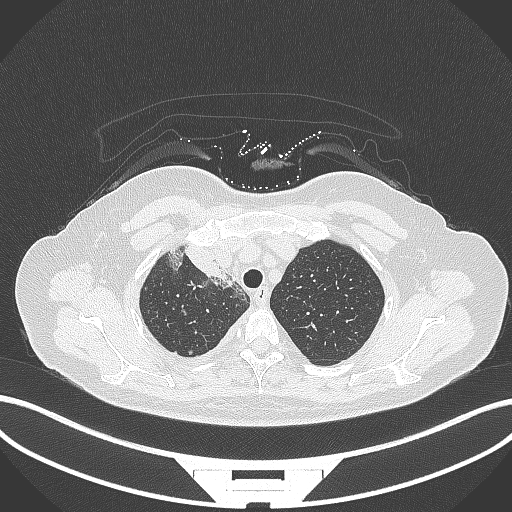
Chest CT, one axial slice. Slice 255 of 305 in the series (ordered by position). Reconstruction kernel B70f. 120 kVp. Lung window (W 1500 / L -600 HU). 512 × 512 image matrix, field of view 400 × 400 mm. Female patient, age 52 years. Case-level facts recorded for this patient, not image findings: clinical TNM (as recorded): T3 N1 M1.
Outlined on this slice (rectangle marked by the reading radiologist):
- lung tumour (recorded histology: adenocarcinoma): bounding box <169,243,226,282> (left, top, right, bottom; pixels)